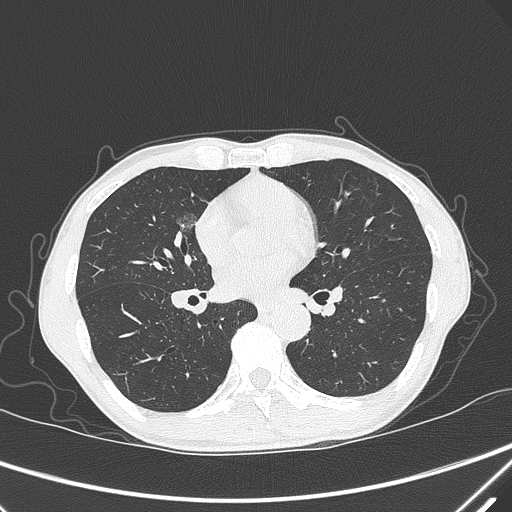
Chest CT, one axial slice. Slice 162 of 339 in the series (ordered by position). 120 kVp. Lung window (W 1500 / L -600 HU). 1 mm slice thickness. 512 × 512 image matrix, field of view 350 × 350 mm. Patient: male, 67 years. From the clinical record (not read from this slice): clinical TNM (as recorded): T1c N0 M0; histopathological grade: G1-2.
Structures marked on this image (bounding box drawn by a radiologist):
- lung tumour (recorded histology: adenocarcinoma): bounding box [x1, y1, x2, y2] px = [169, 205, 208, 238]